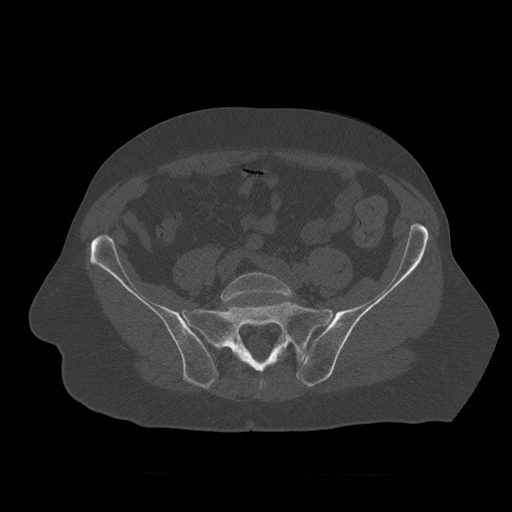
CT including the spine, one axial slice. Slice 239 of 450 in the series (ordered by position). Reconstruction kernel STANDARD. 120 kVp. Bone window (W 1800 / L 400 HU). 512 × 512 image matrix. Patient age 75 years. From the clinical record (not read from this slice): primary cancer: prostate.
Annotated regions visible in this slice (semi-automatically segmented with operator editing):
- L5 vertebra: bounding box [x1, y1, x2, y2] px = [221, 272, 295, 303]